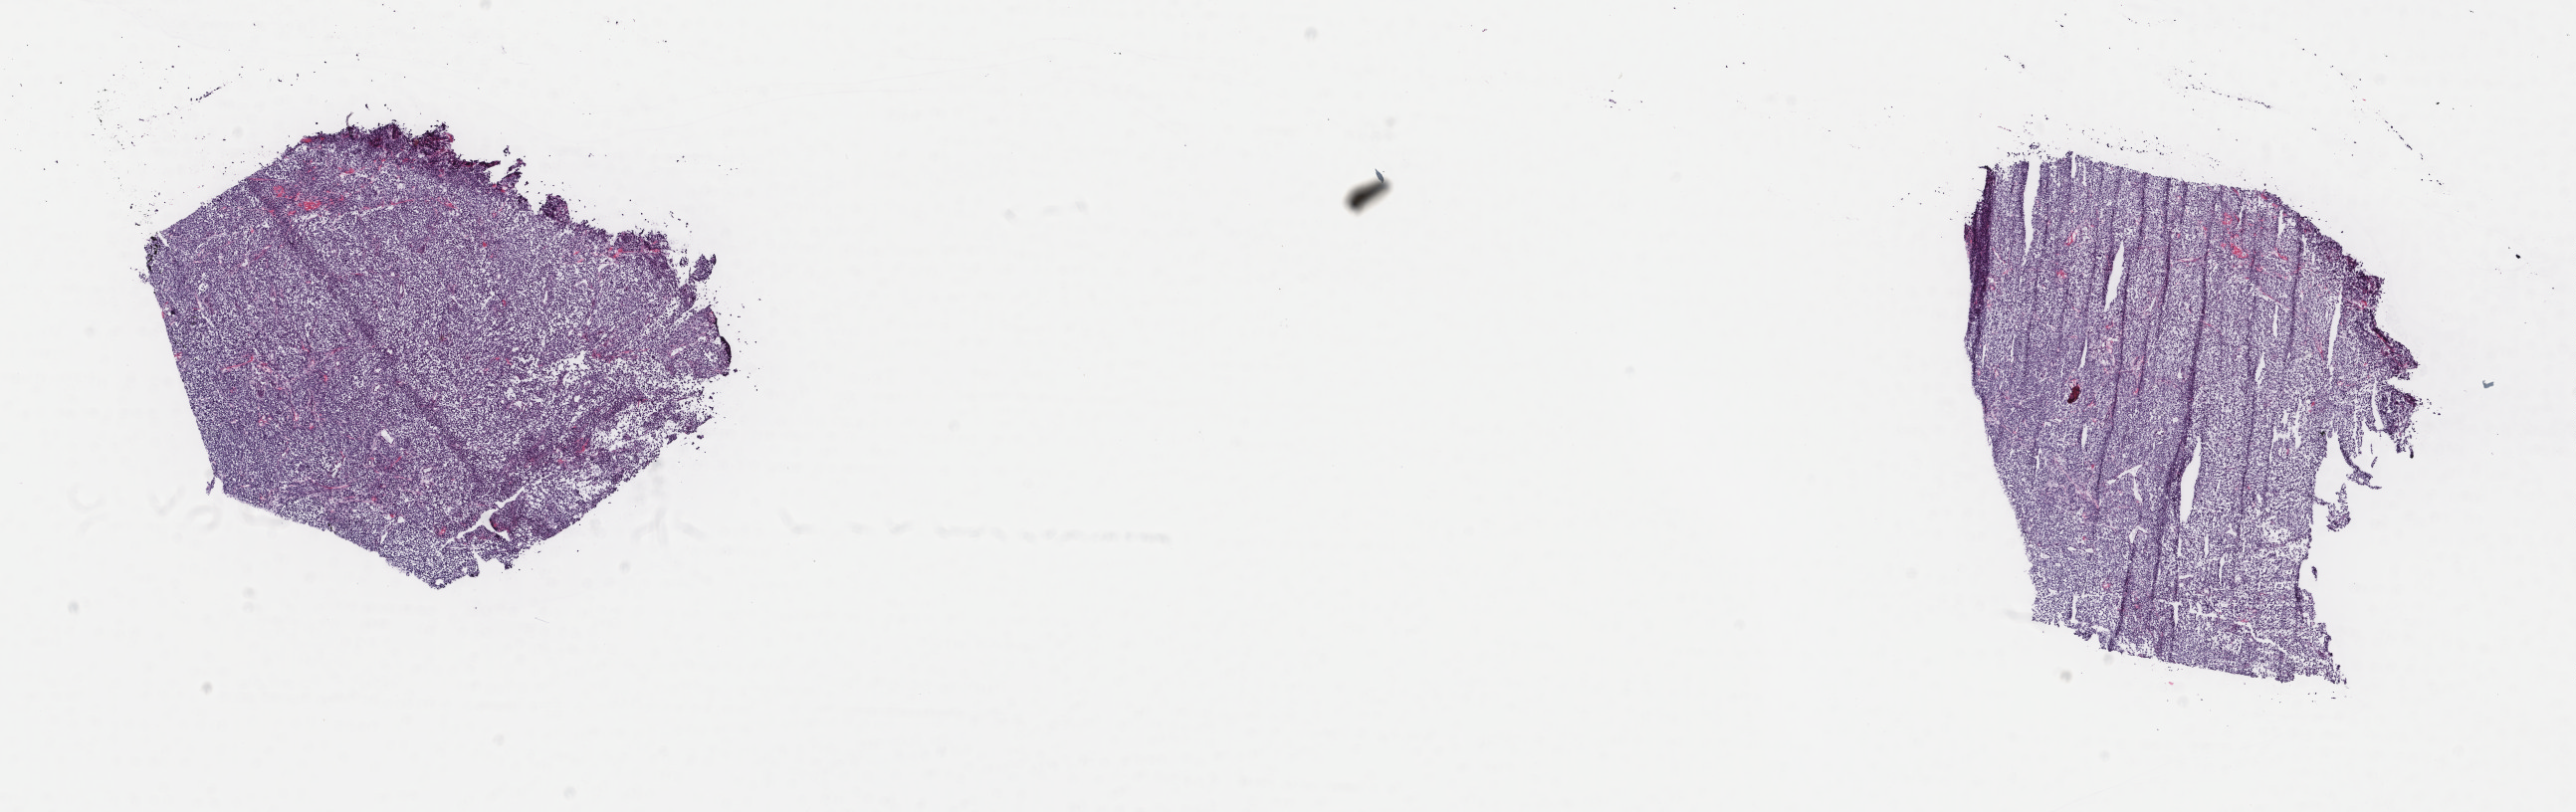
Digitized H&E tissue section (whole slide), whole scanned area (about 20.5 x 6.5 mm, from a 40x scan) shown as a low-resolution overview, frozen section, metastatic tumour sample, sampled site: connective, subcutaneous and other soft tissues of thorax. Male patient; age at initial diagnosis 40 years. Pathologist review of this section (percent, as recorded): tumour cells 100%, tumour nuclei 98%, normal cells 0%, stromal cells 0%, necrosis 0%. Inflammatory infiltration, as recorded: lymphocyte infiltration 0%, monocyte infiltration 0%, neutrophil infiltration 0%.
This section: metastatic tumour tissue. Patient diagnosis: Malignant melanoma, NOS.